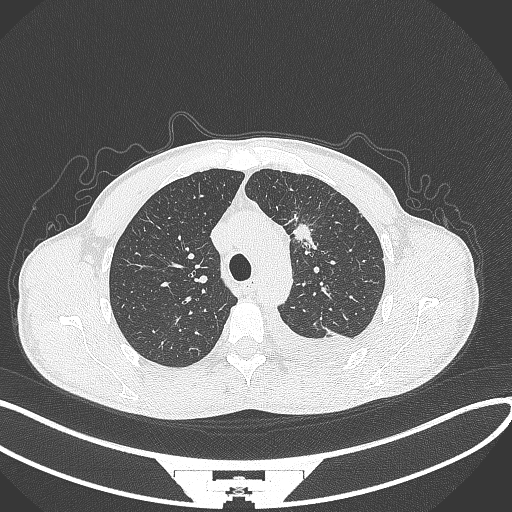
Chest CT, one axial slice. Slice 246 of 371 in the series (ordered by position). Lung window (W 1500 / L -600 HU). 512 × 512 image matrix, field of view 400 × 400 mm. Male patient, age 49 years. Case-level facts recorded for this patient, not image findings: clinical TNM (as recorded): T1c N1 M1.
Outlined on this slice (bounding box drawn by a radiologist):
- lung tumour (recorded histology: adenocarcinoma): bounding box <286,217,315,250> (left, top, right, bottom; pixels)